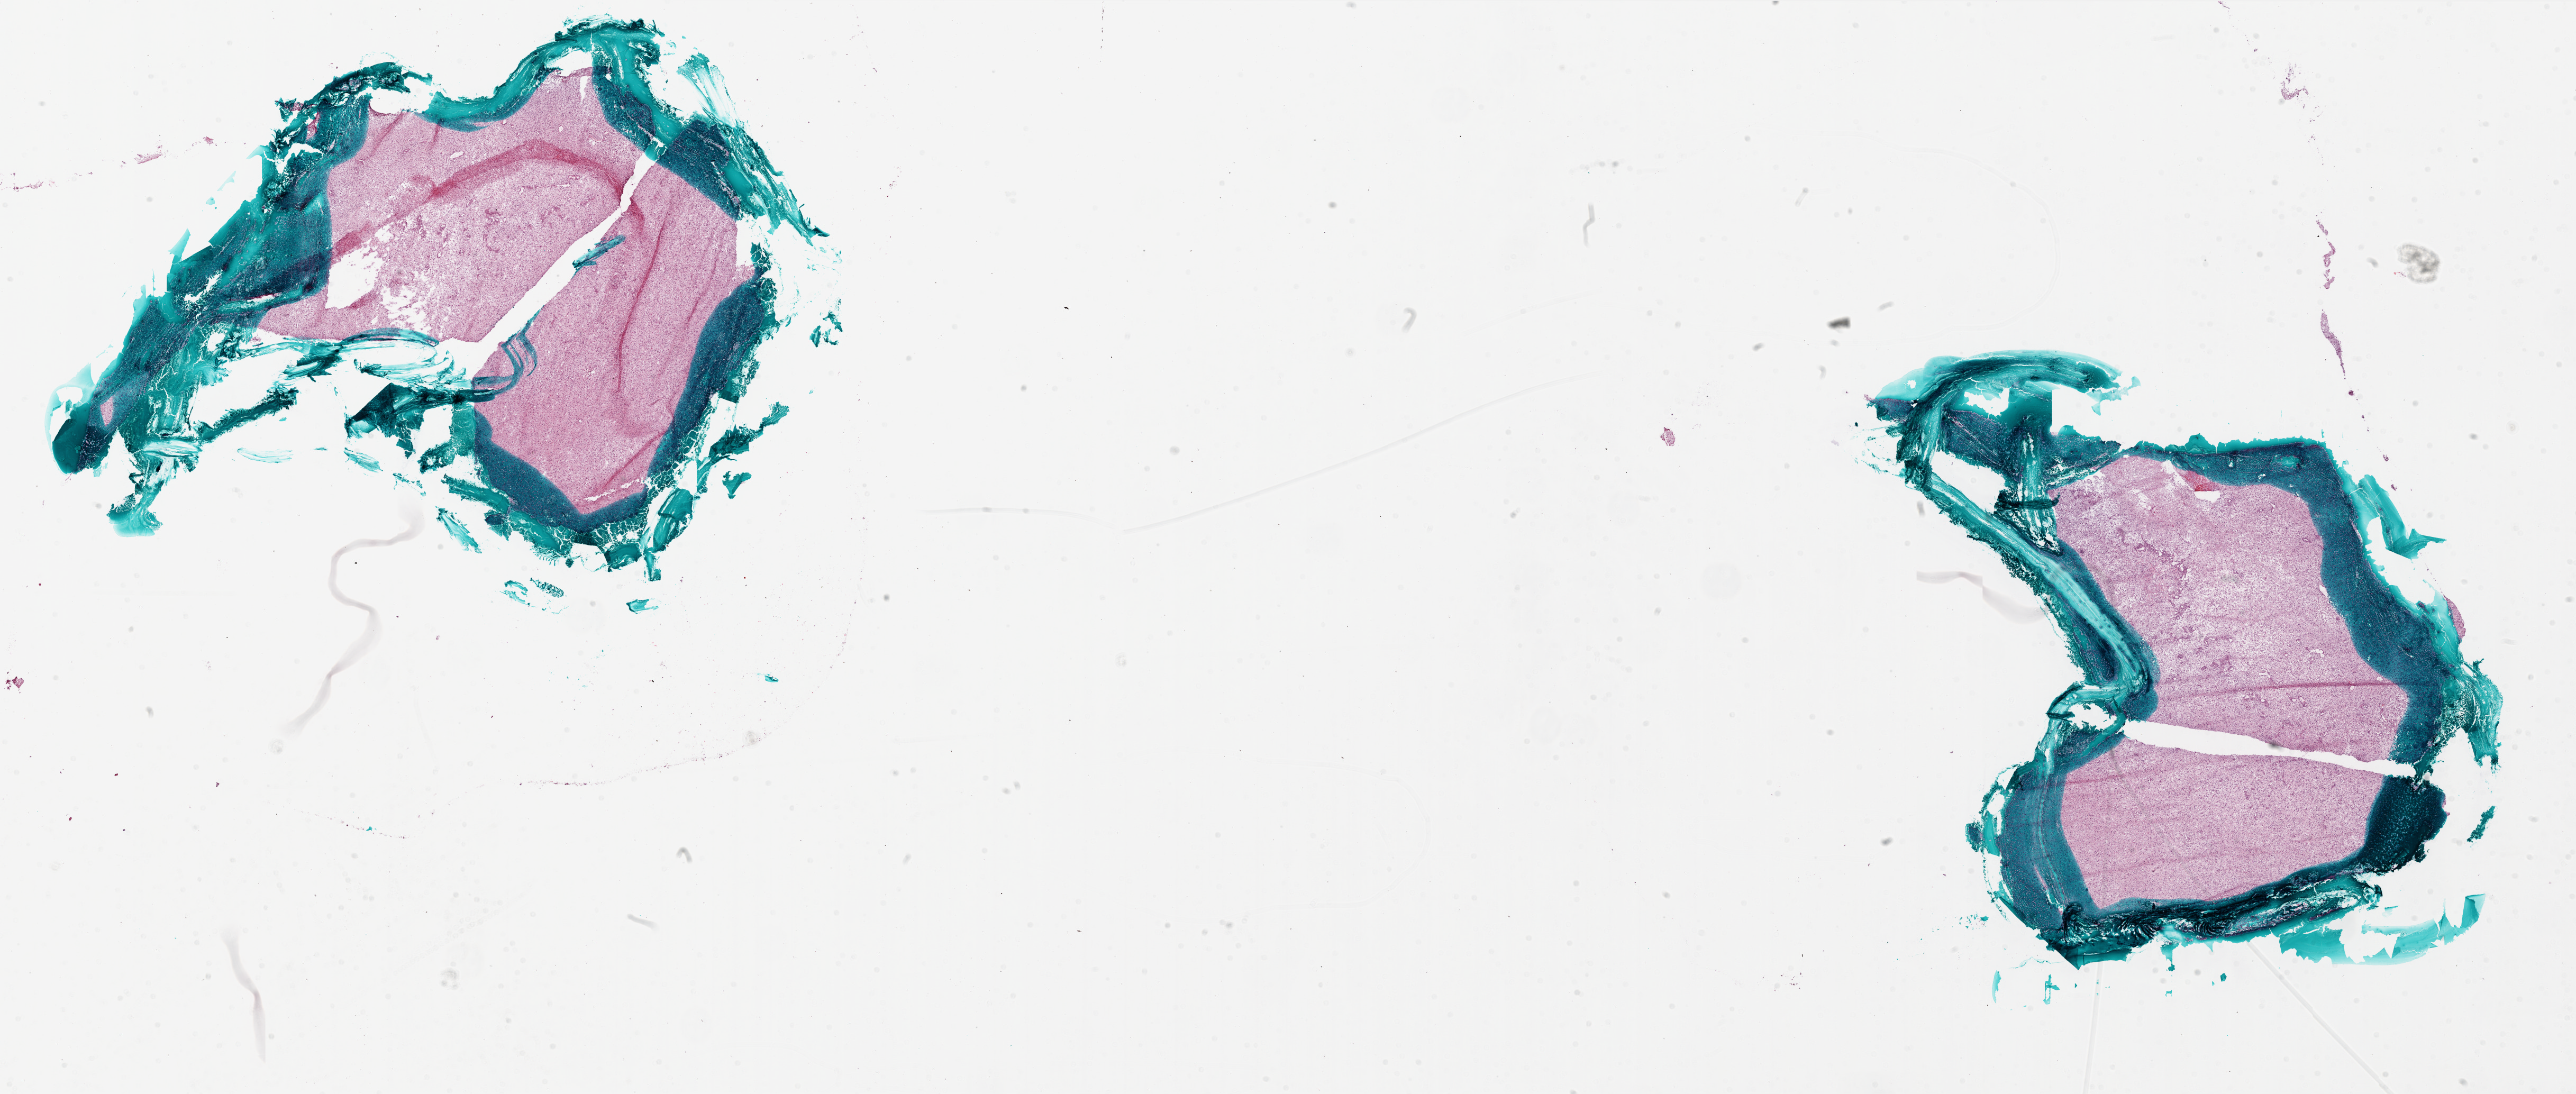
H&E-stained whole-slide image — shown as a low-resolution overview of the whole scanned area (about 39.0 x 16.5 mm, from a 20x scan); frozen section; primary tumour sample from the brain. Male, age 53 years at initial diagnosis. Composition of this section per pathologist review: tumour cells 95%, tumour nuclei 100%, normal cells 0%, stromal cells 0%, necrosis 5%.
* diagnosis: Glioblastoma